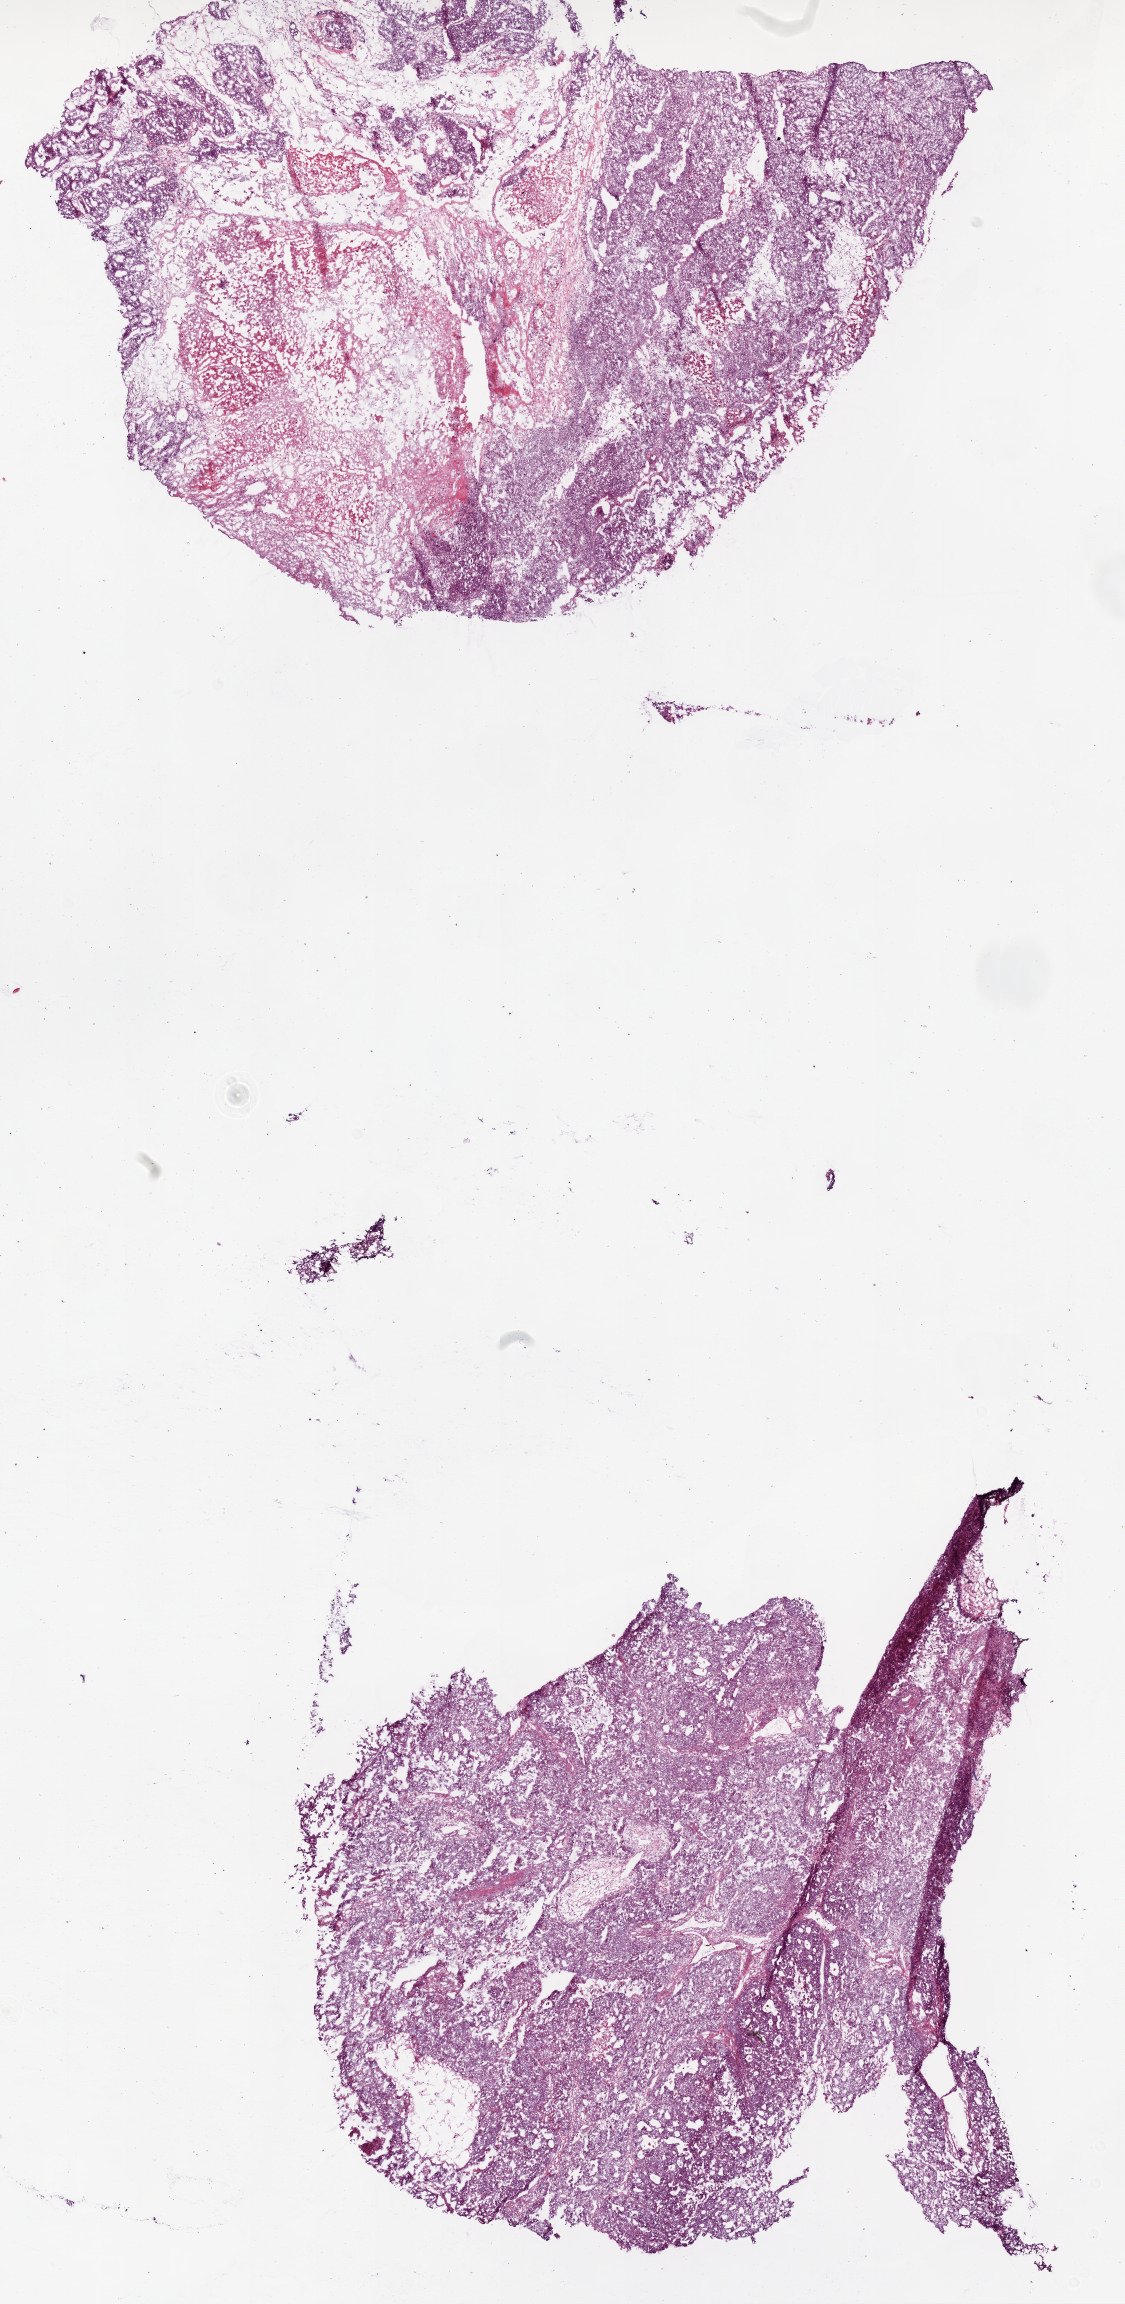
Whole-slide histology image, Hematoxylin and eosin (H&E) stained — low-resolution overview of the scanned area, about 9.0 x 18.5 mm (acquisition: 20x scan), frozen section, sample: primary tumour, ovary. Female patient; age at initial diagnosis 75 years. Histologic grade: G3 (poorly differentiated). Pathologist review of this section (percent, as recorded): tumour cells 70%, tumour nuclei 80%, normal cells 0%, stromal cells 30%, necrosis 0%. Infiltration values recorded for this section: lymphocyte infiltration 1%.
Pathologic diagnosis: Serous cystadenocarcinoma, NOS. FIGO stage: IIIC.